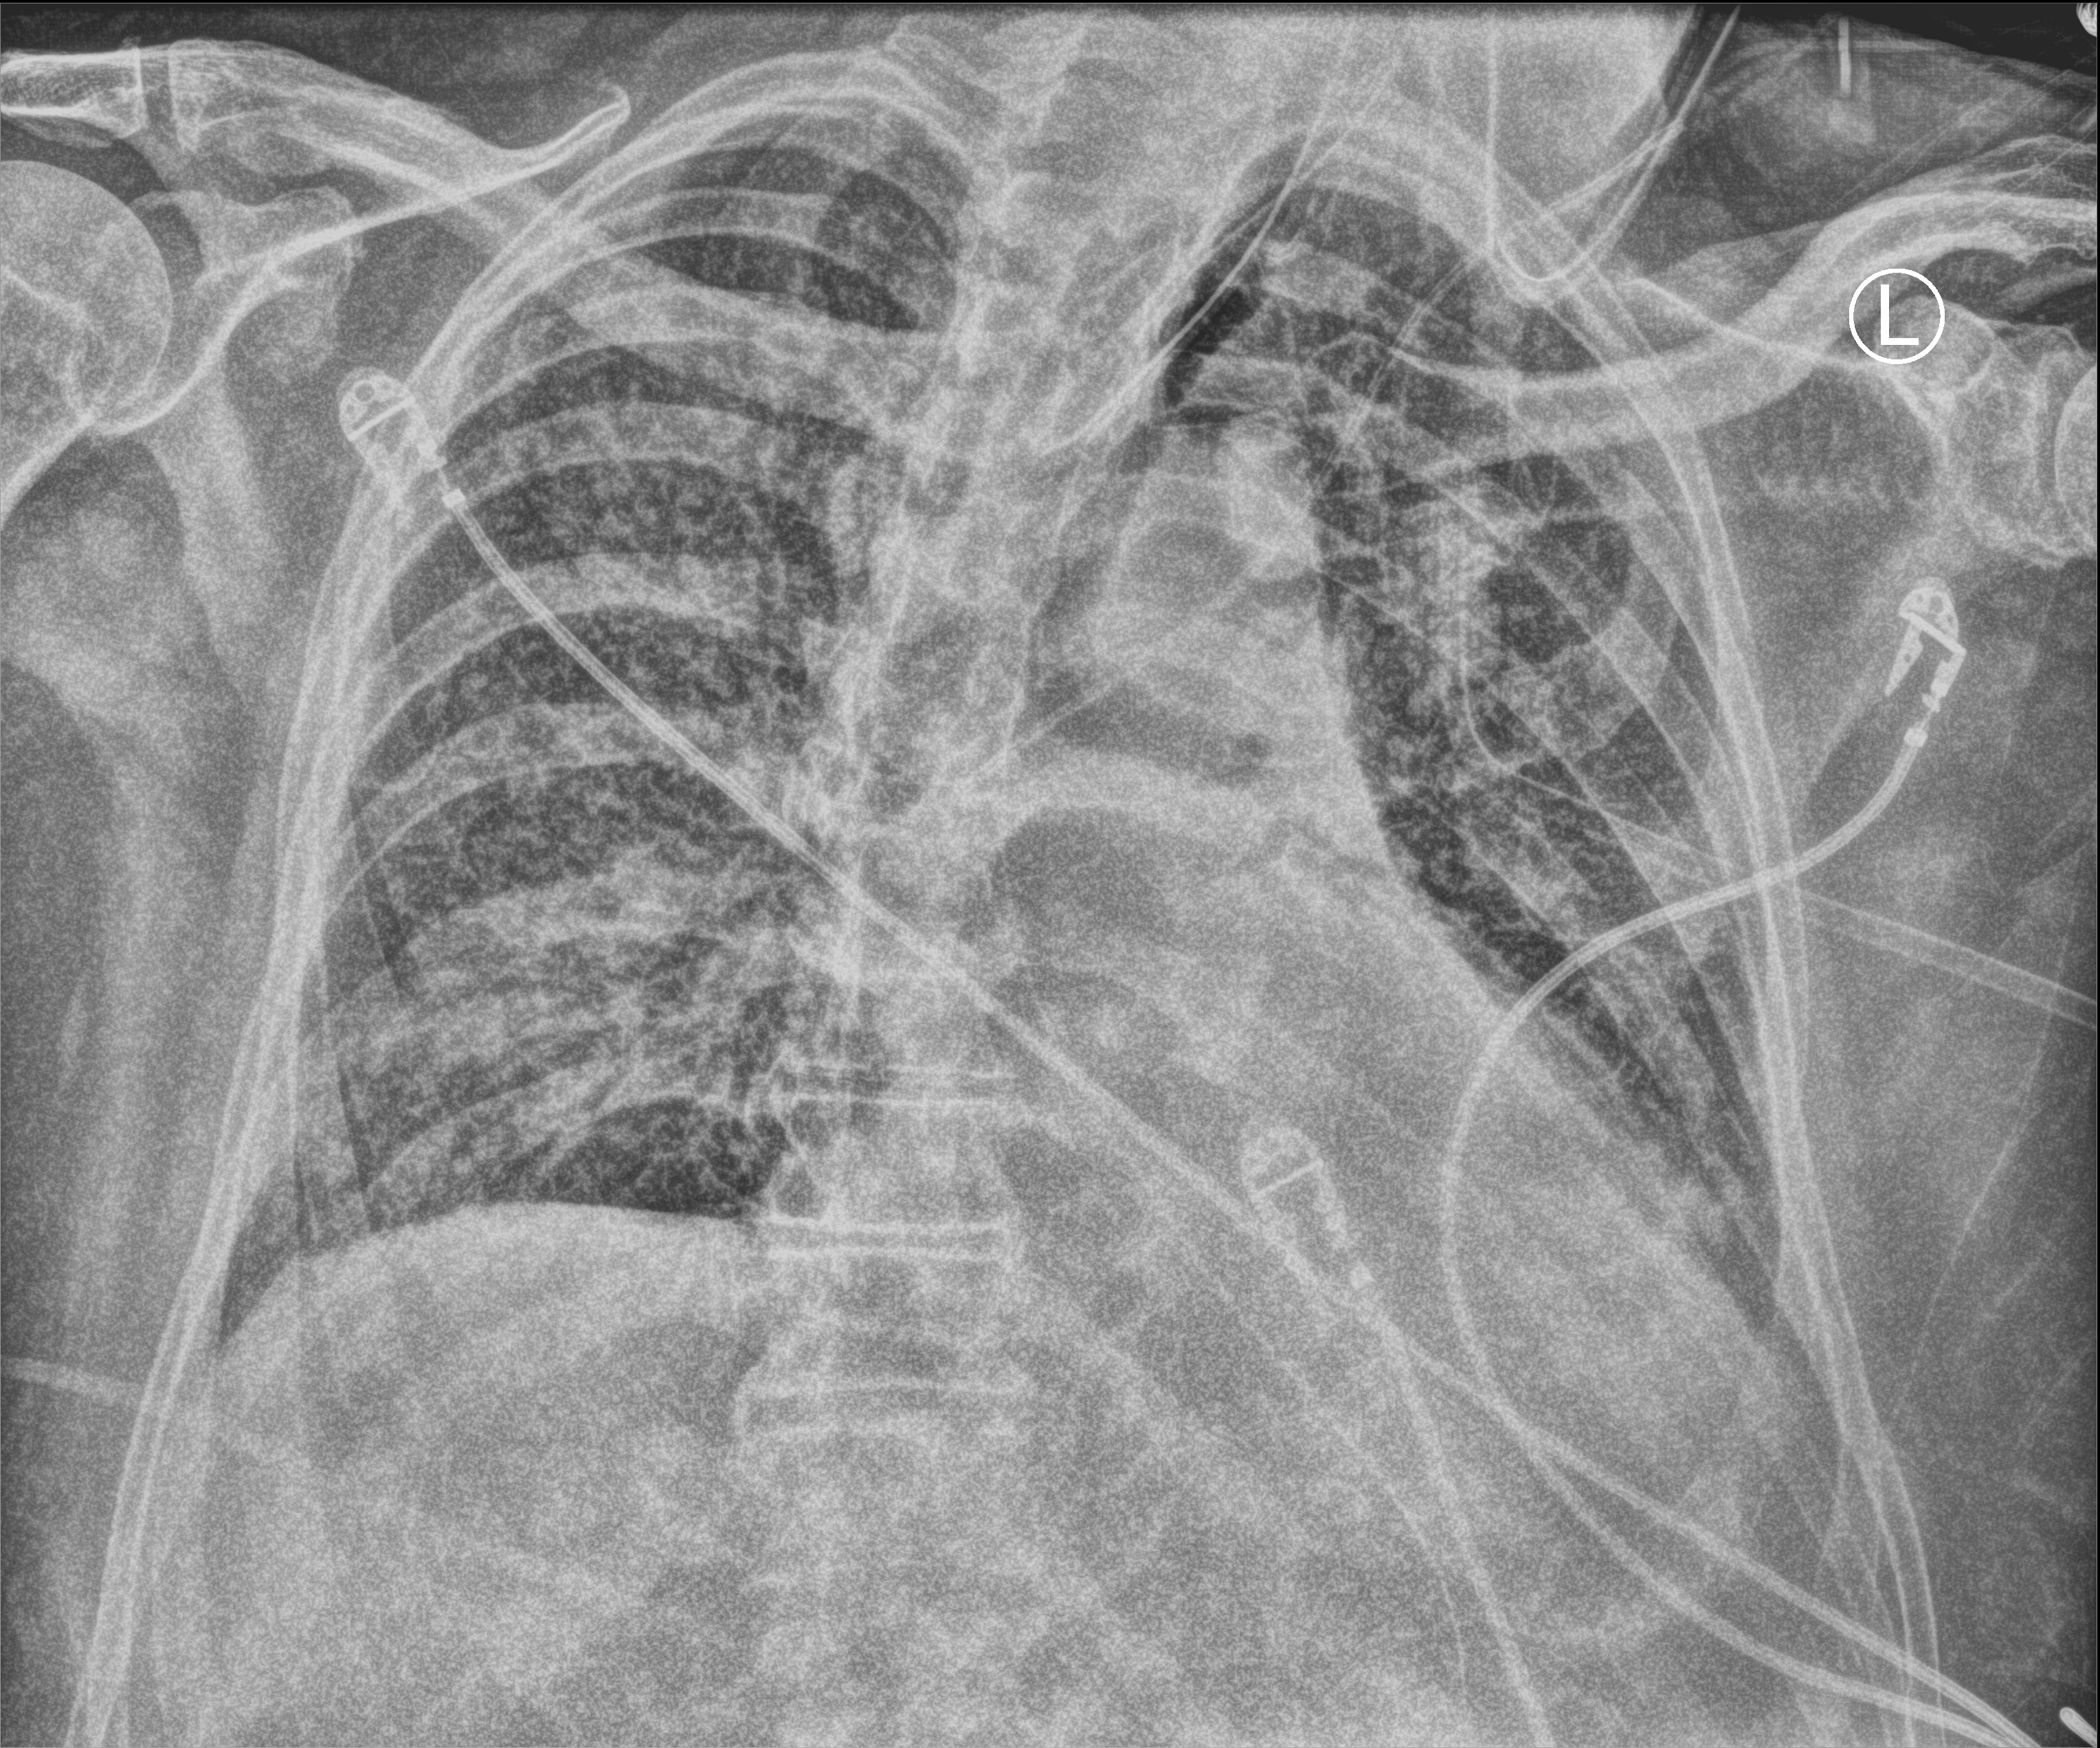
Portable chest radiograph; anteroposterior (AP) projection. Patient hospitalised with COVID-19; male, aged 75–90 years.
From the hospital-stay record, not from the radiograph (when in the stay this image was taken is not recorded):
- other chronic lung disease (admission record): no